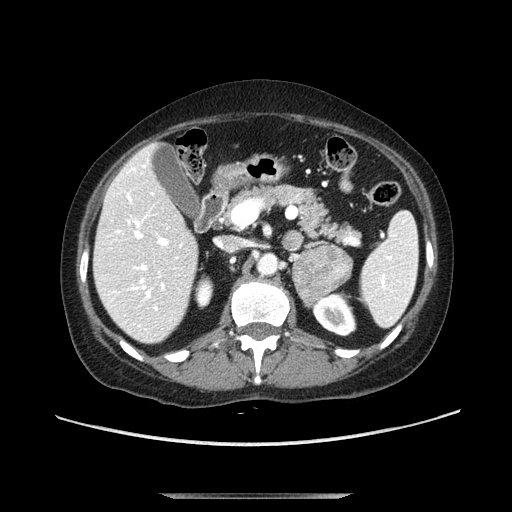
Contrast-enhanced abdominal CT, one axial slice. Position 60 of 107 along the scan axis. Soft-tissue window (W 400 / L 40 HU). 2.5 mm slice thickness. 512 × 512 image matrix, field of view 380 × 380 mm. Female patient. Case-level facts recorded for this patient, not image findings: diagnosis: adrenocortical carcinoma; tumour side: left adrenal; tumour size at pathology: 7.5 cm; Ki-67 index: 9 %; stage (as recorded): 3.
Outlined on this slice (semi-automatically segmented with operator editing):
- mass: bounding box [x1, y1, x2, y2] px = [292, 244, 353, 305]